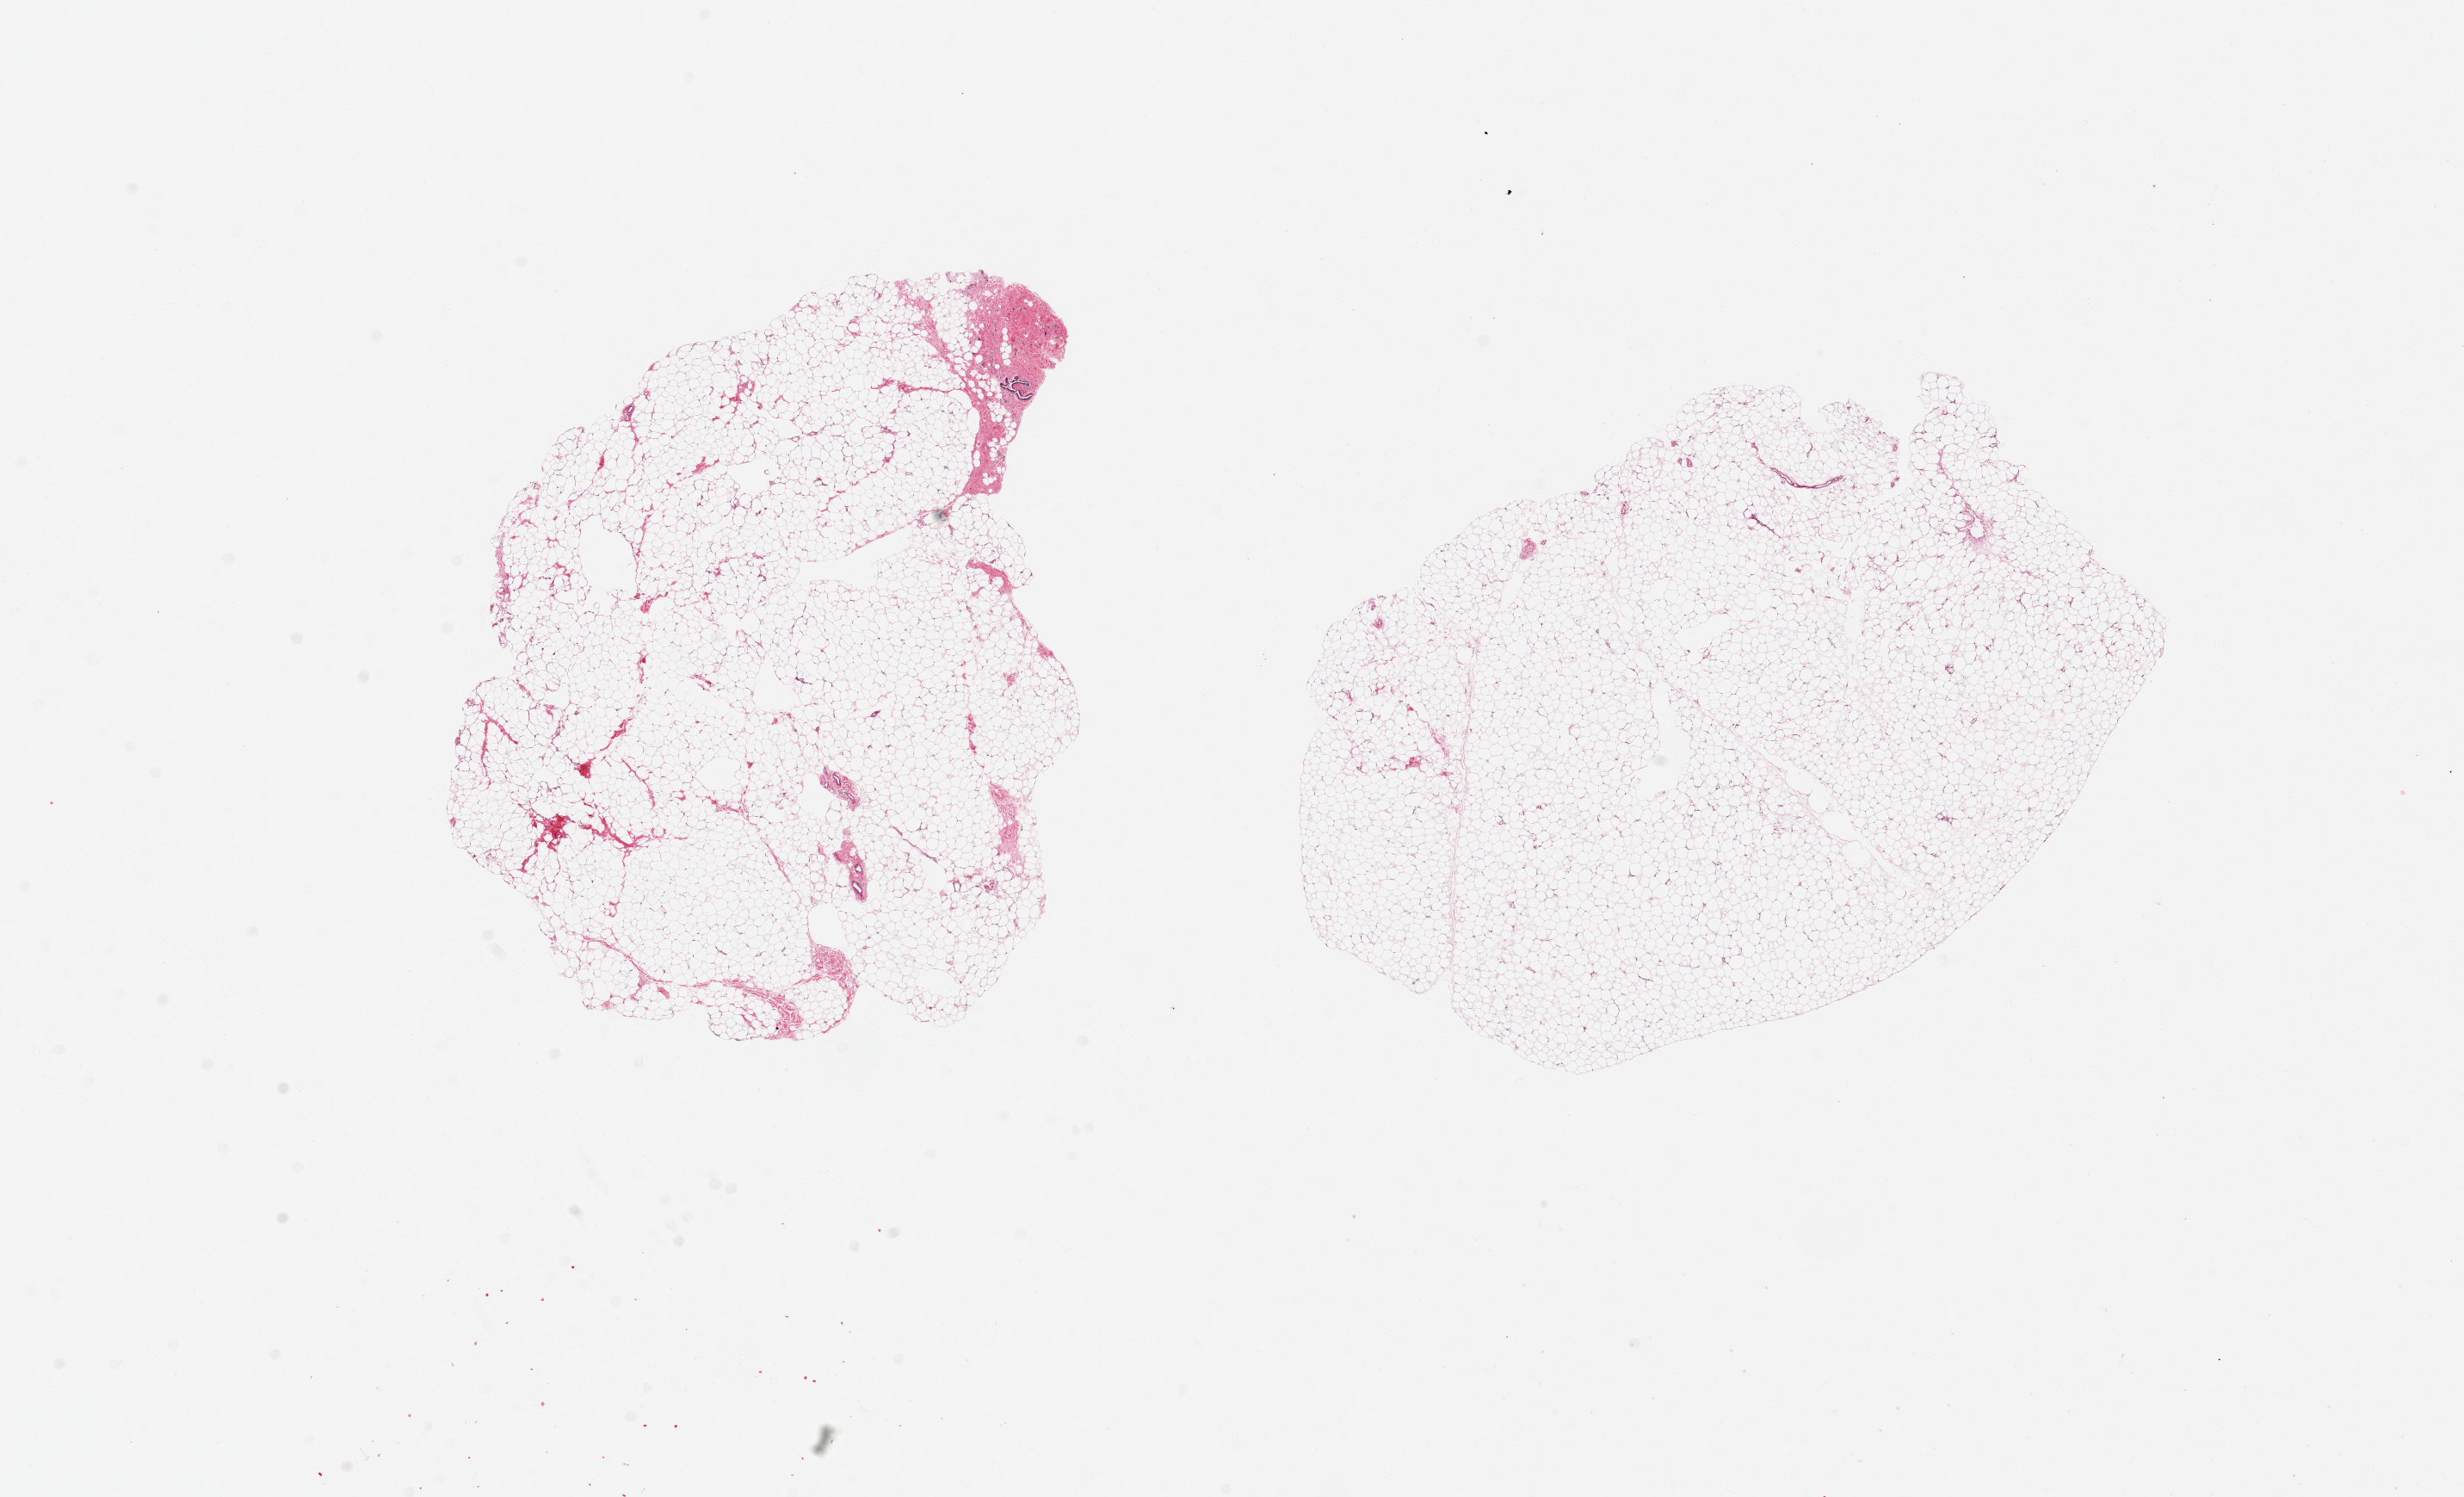
H&E whole-slide image, brightfield — a low-resolution overview of the entire scanned area, about 22.6 x 13.8 mm (slide scanned at 20x), PAXgene-fixed paraffin-embedded (PFPE) section, sampled site (target tissue): breast, donor tissue sample. Male donor.
Reviewer comment on this tissue sample: 2 pieces, 7x6 & 8x6mm; minute (~0.3mm) single ductal element noted, rest is fat.